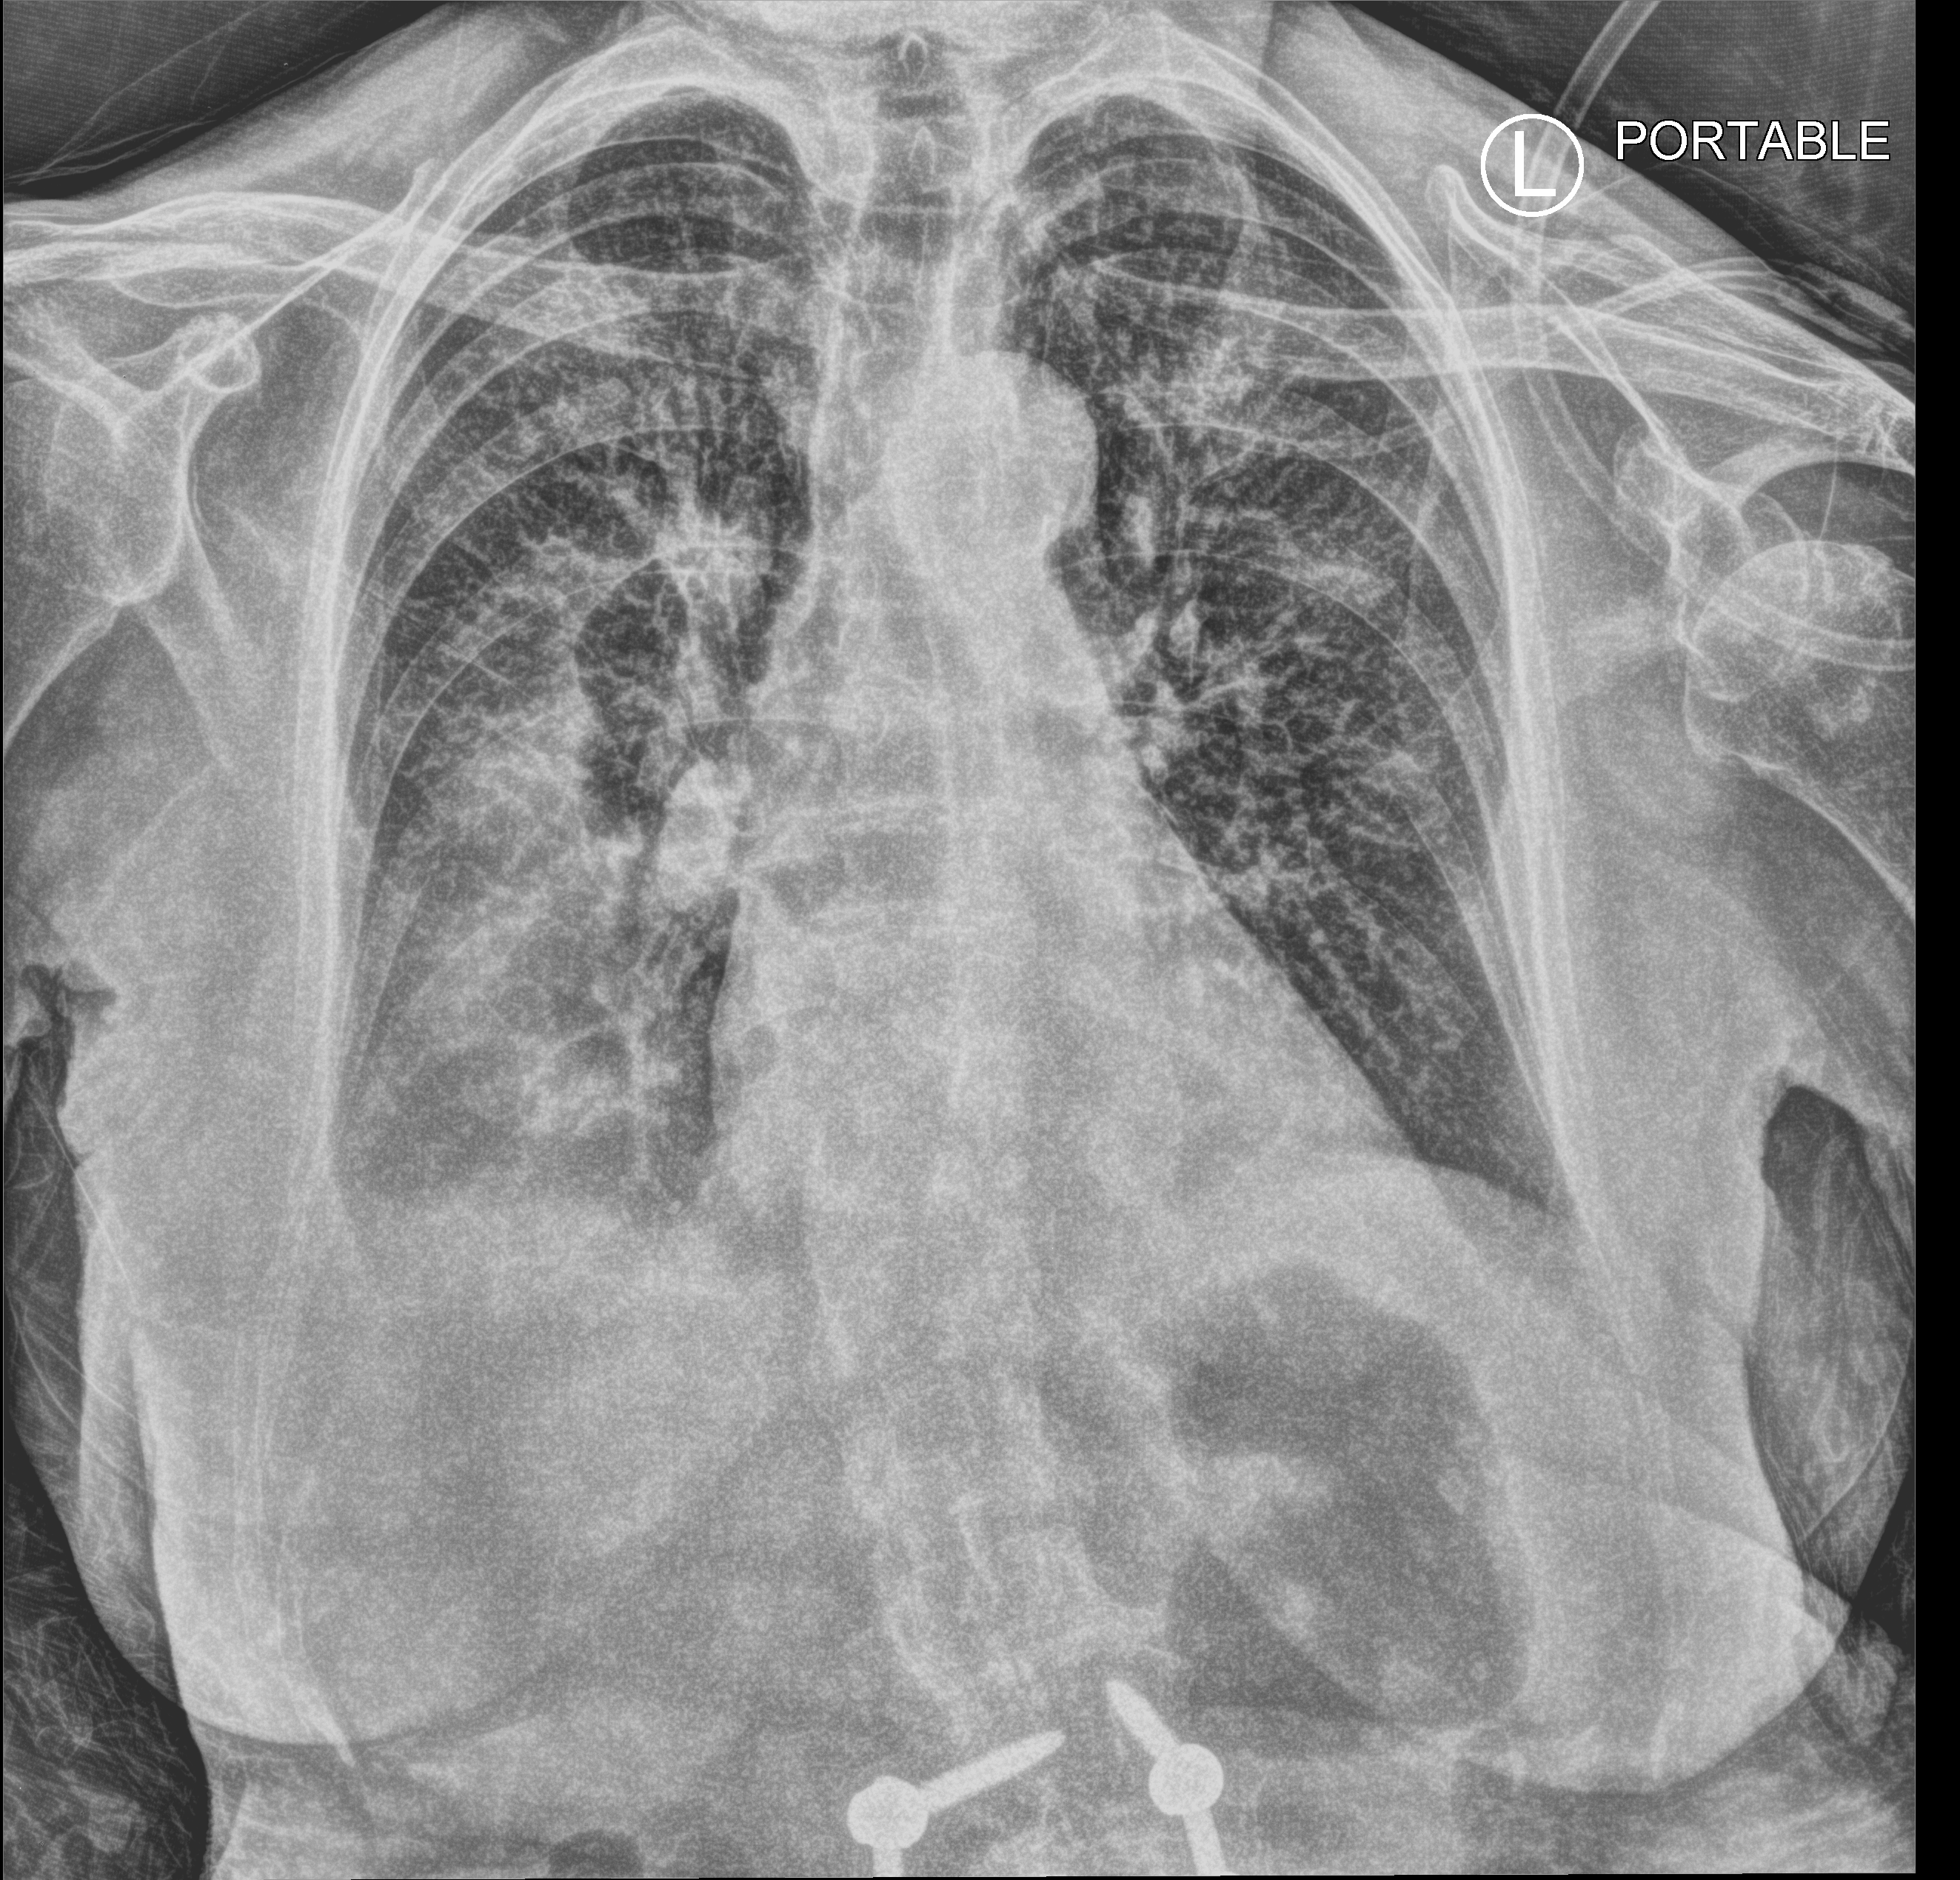
Chest X-ray (portable), anteroposterior (AP) projection. Female patient hospitalised with COVID-19, age 60–74 years.
Admission-level facts for this patient (not findings on this image; timing relative to this image not recorded): admitted to intensive care during this hospital stay: no; length of hospital stay: 13 days; mechanically ventilated during this hospital stay: no.